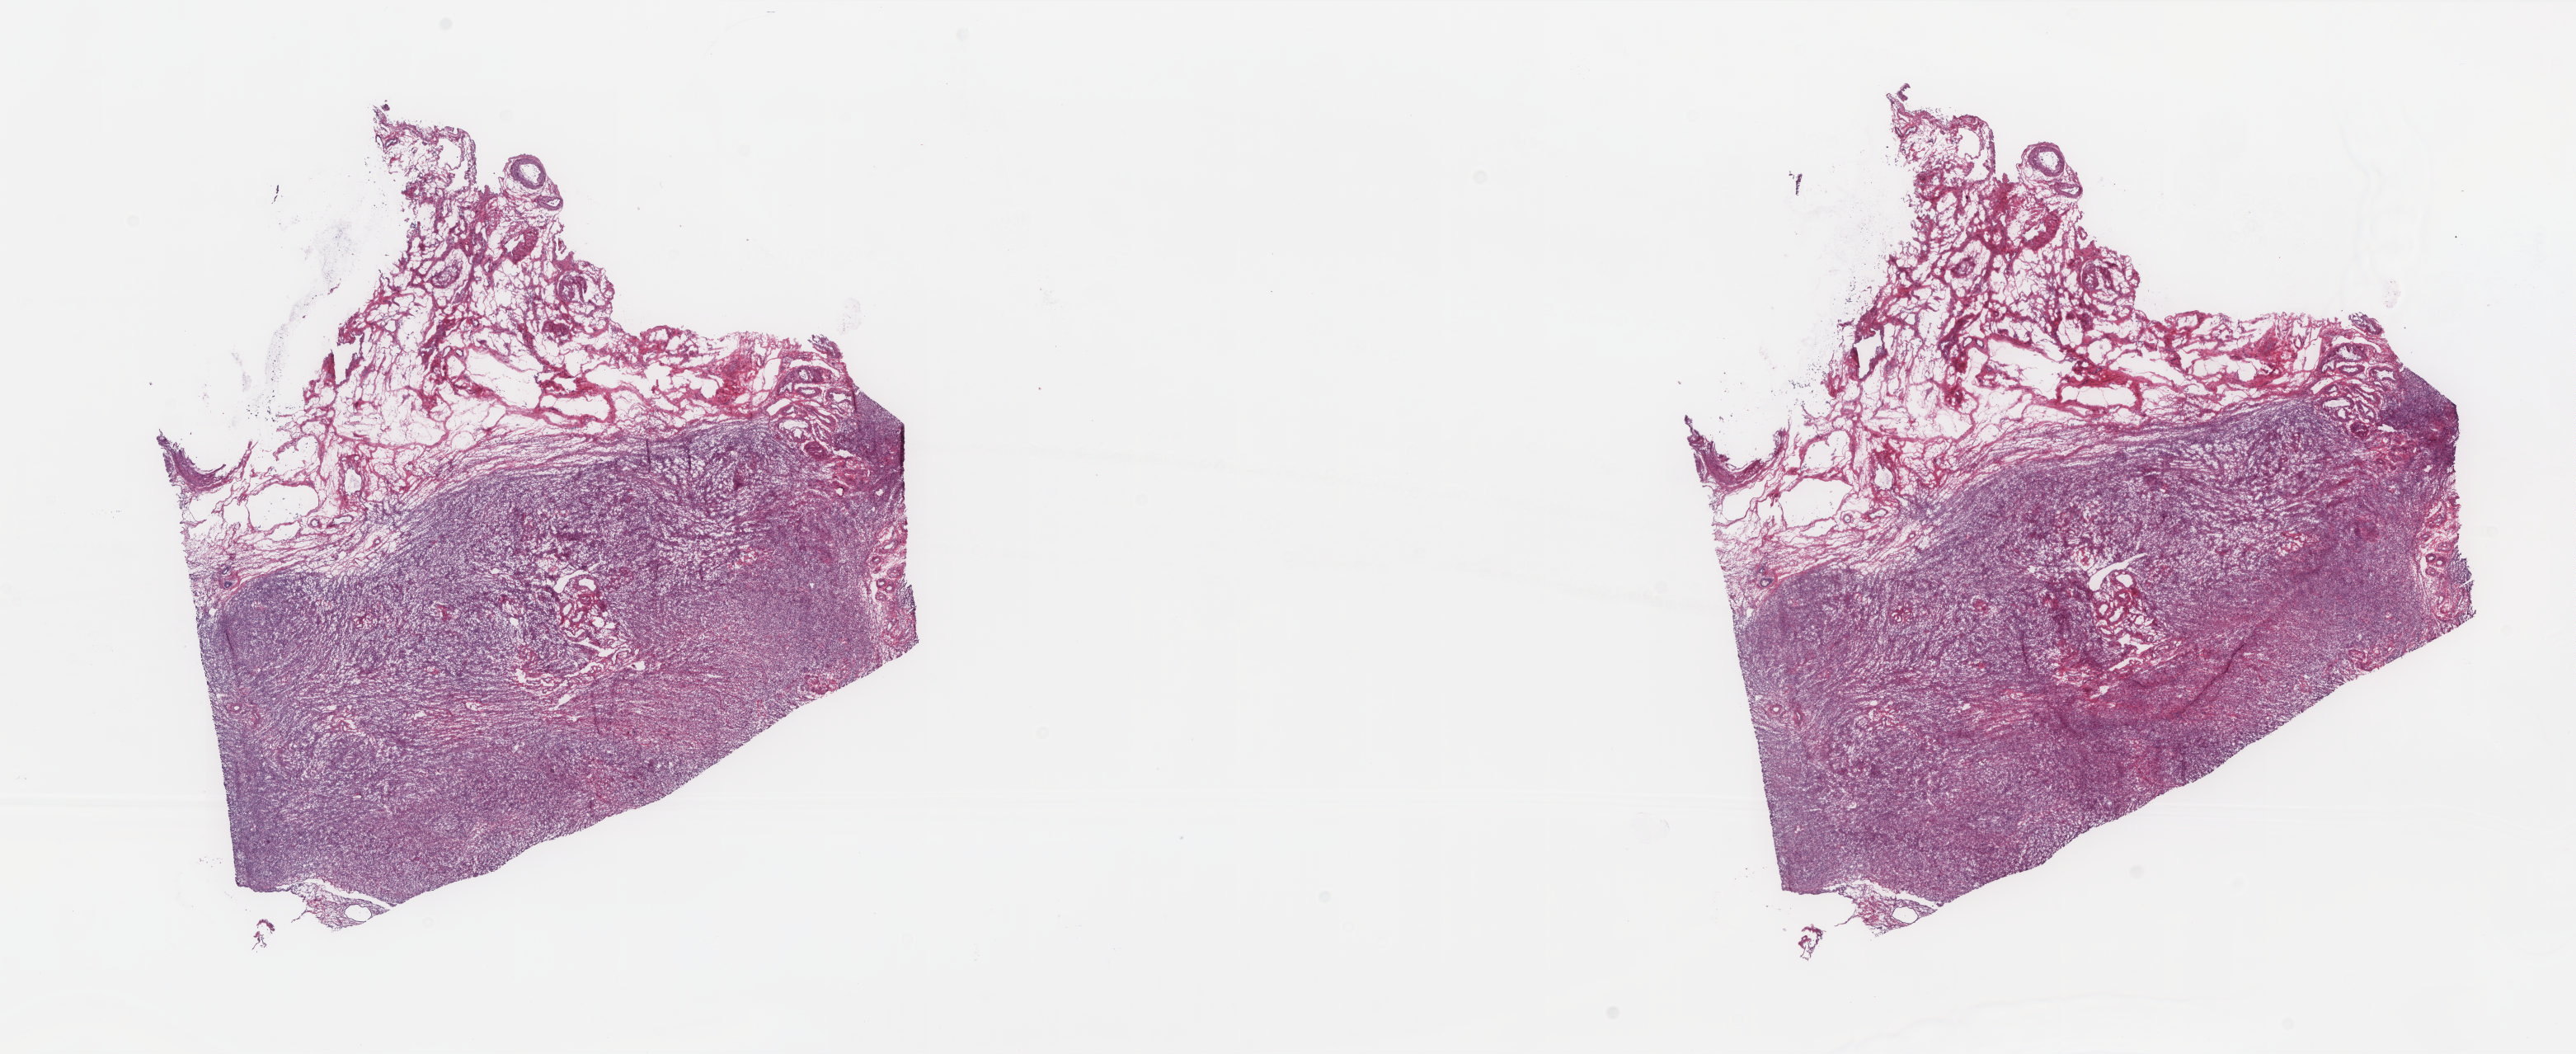
Whole-slide histology image, H&E — low-resolution overview of the scanned area, about 25.0 x 10.2 mm (from a 20x scan); frozen section from the top of the tissue portion; solid tissue normal (non-tumour tissue) sample from the uterus. Female patient; age at initial diagnosis 82 years. Slide review estimates, as recorded: tumour cells 0%, tumour nuclei 0%, normal cells 100%, stromal cells 0%, necrosis 0%. Infiltration values recorded for this section: lymphocyte infiltration 1%, monocyte infiltration 0%, neutrophil infiltration 0%.
This section: solid tissue normal (non-tumour) sample from the same patient. Patient diagnosis: Serous cystadenocarcinoma, NOS (endometrium).